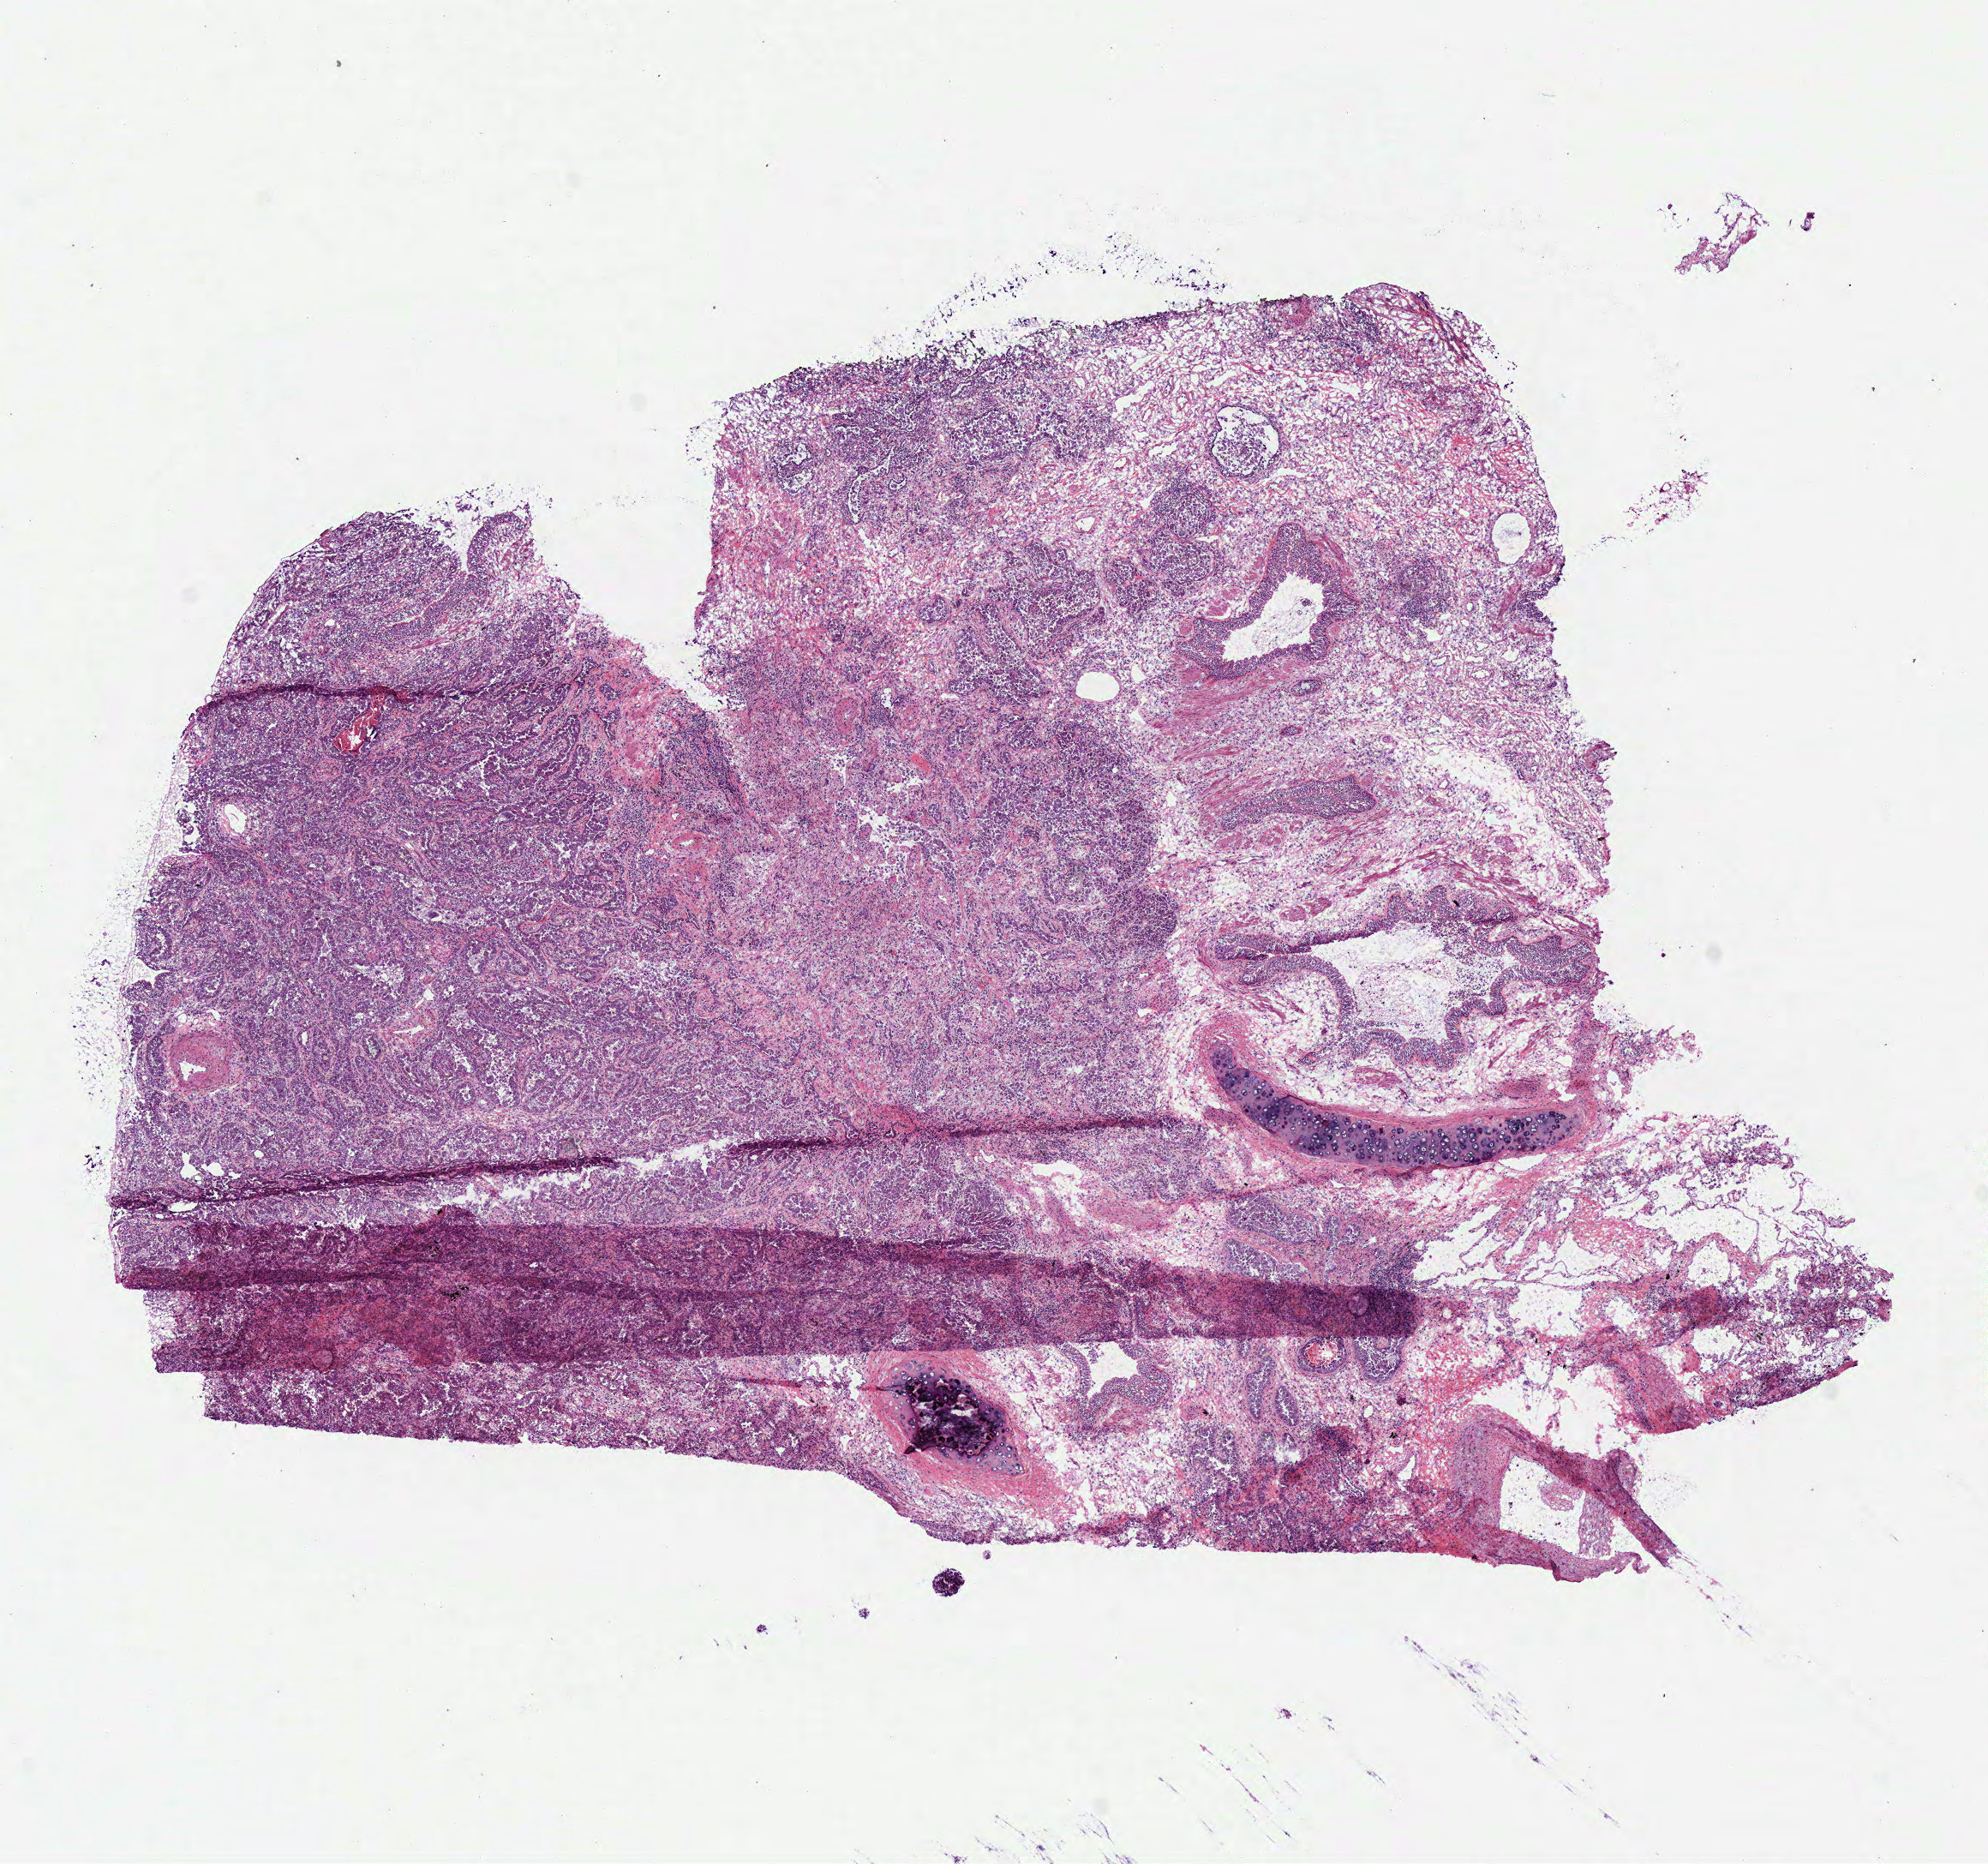
Hematoxylin and eosin (H&E) stained whole-slide image — a low-resolution overview of the entire scanned area, about 9.1 x 8.6 mm (slide scanned at 40x); frozen section; sample: primary tumour, lung. Patient: female, age at initial diagnosis 67 years. Composition of this section per pathologist review: tumour cells 70%, tumour nuclei 75%, normal cells 29%, stromal cells 0%, necrosis 1%. Infiltration values recorded for this section: lymphocyte infiltration 10%, monocyte infiltration 0%, neutrophil infiltration 0%.
* AJCC pathologic stage: IA
* histologic diagnosis: Adenocarcinoma, NOS (upper lobe, lung)